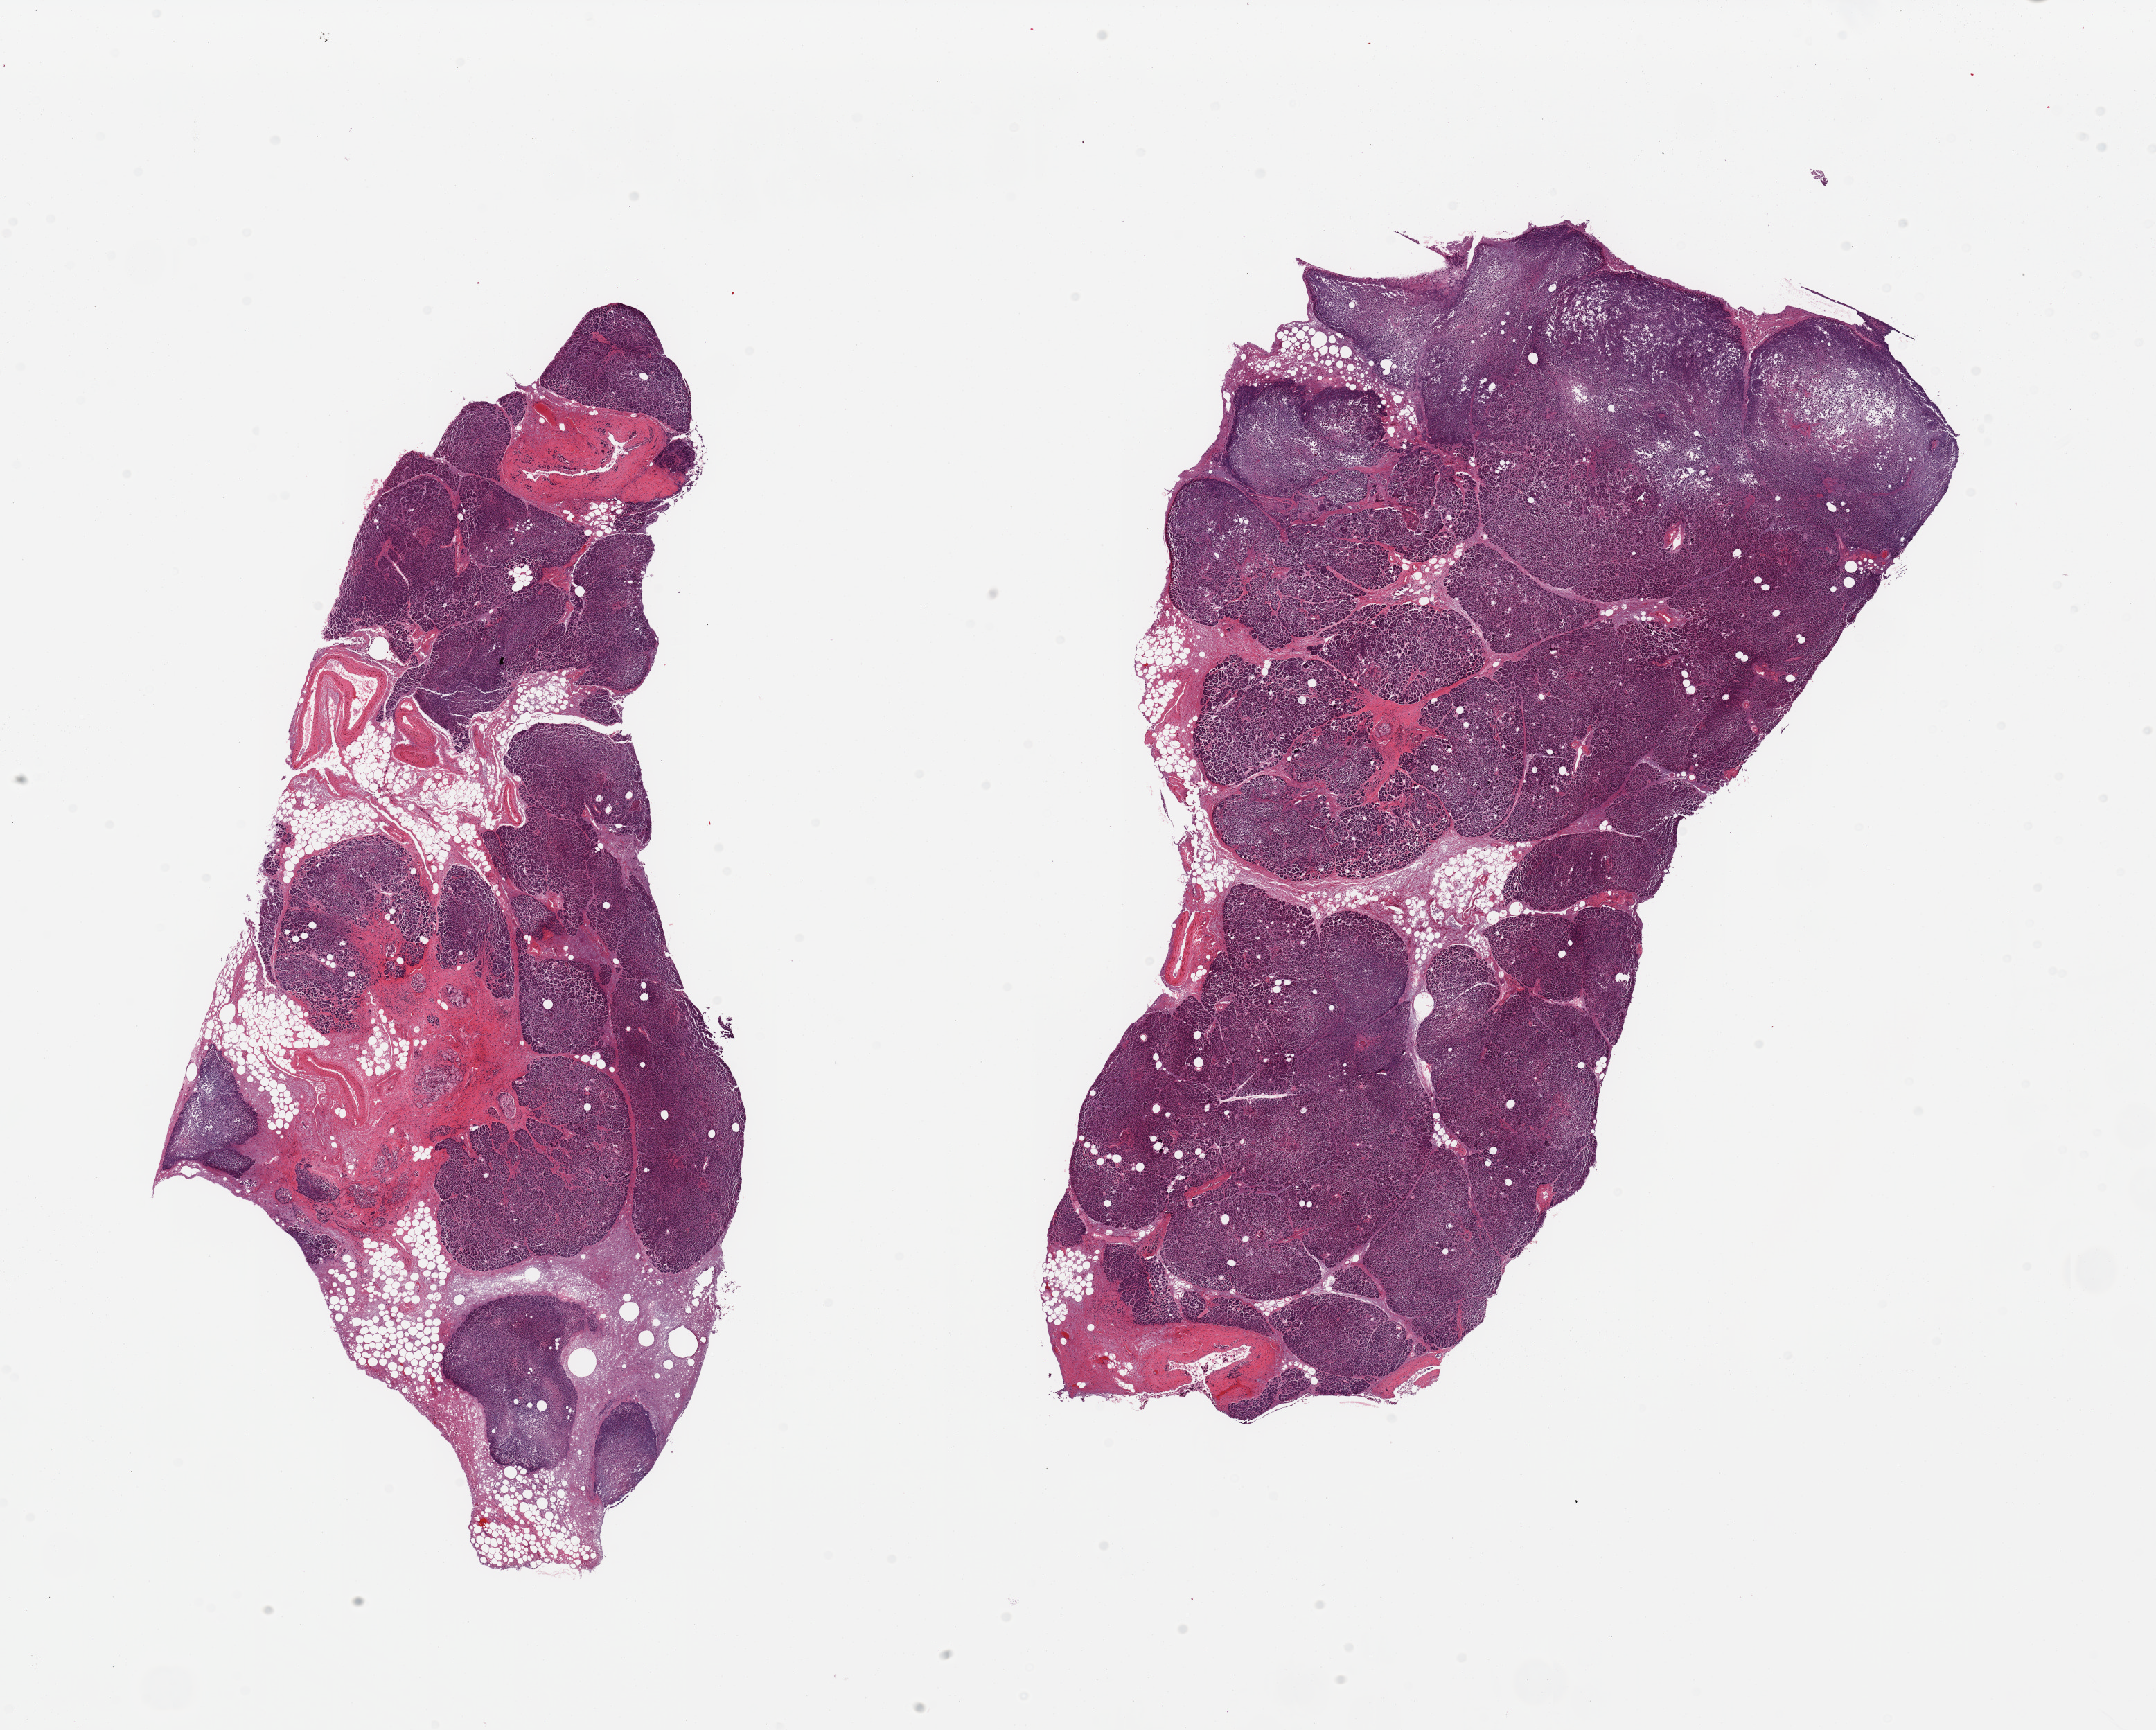
Digitized H&E-stained section — shown as a low-resolution overview of the whole scanned area (about 24.6 x 19.7 mm, from a 20x scan); PAXgene-fixed, paraffin-embedded tissue; target tissue: pancreas; donor tissue sample. Donor: male.
Reviewer comment on this tissue sample: 2 pieces; some areas have less autolysis, '2'; 10 and 40% internal fat; limited value.